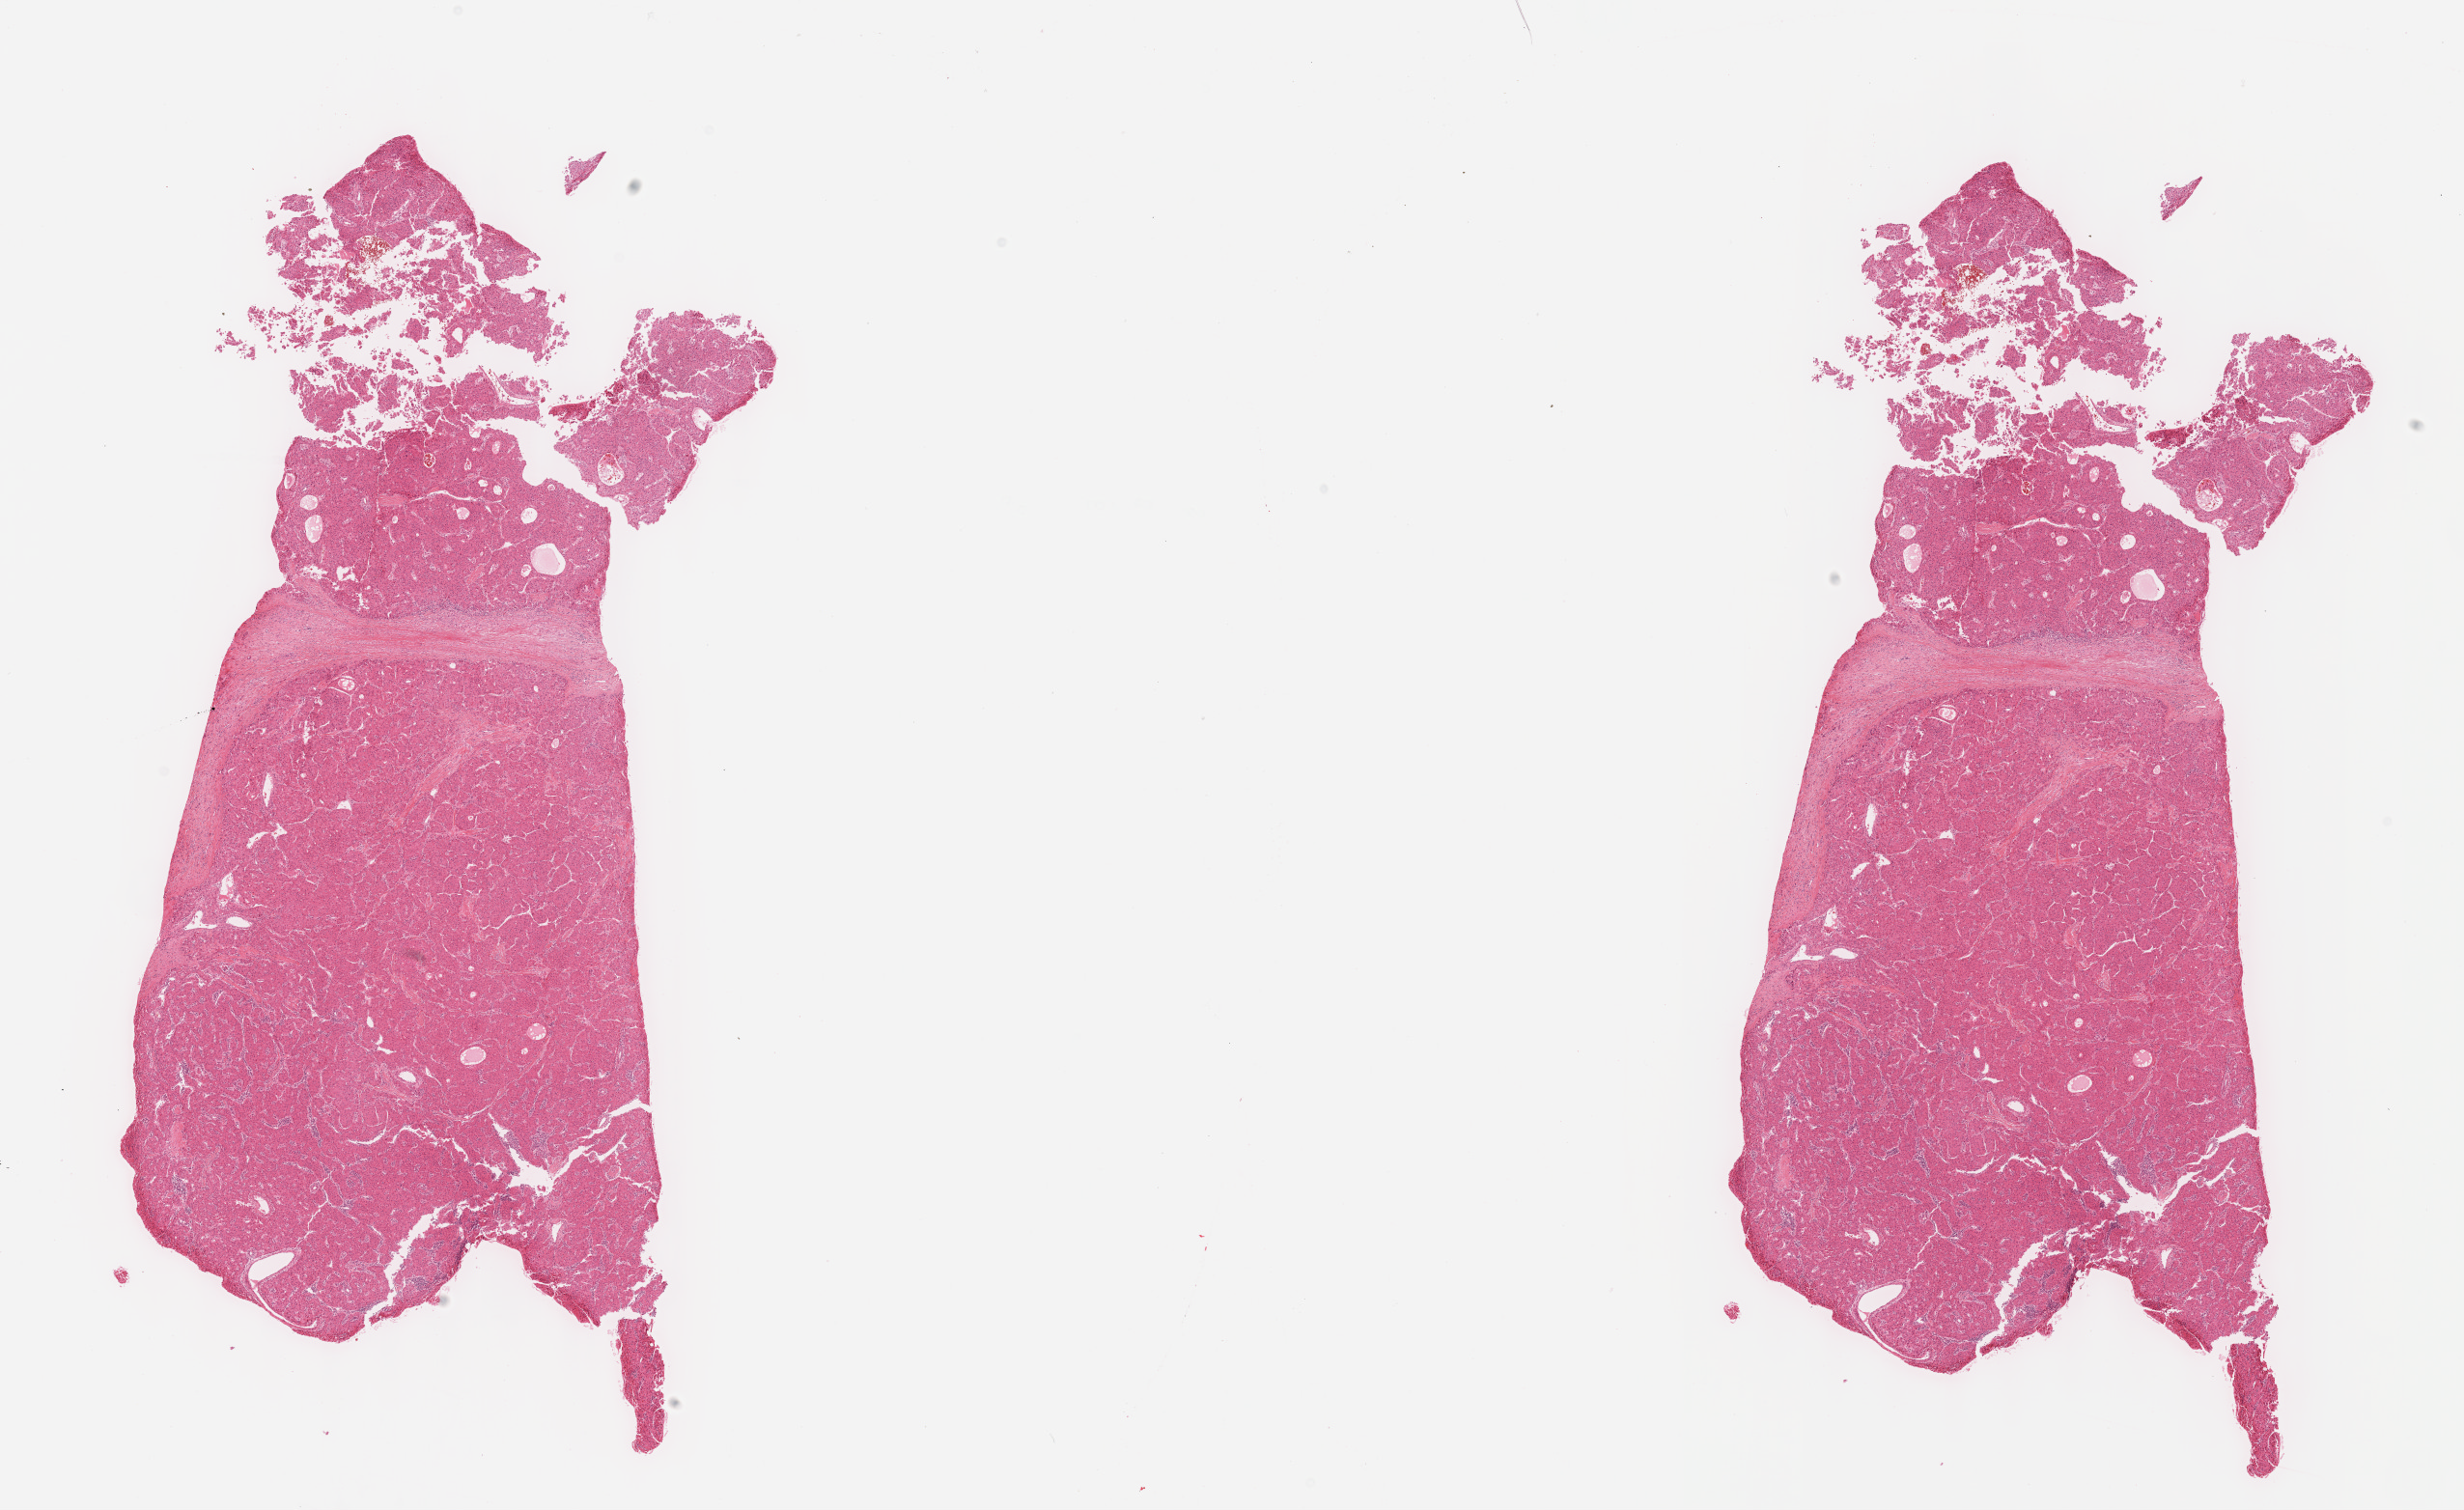
H&E whole-slide image — a low-resolution overview of the entire scanned area, about 20.6 x 12.6 mm, FFPE section, primary tumour sample from the liver. Male patient; age at initial diagnosis 58 years. Histologic grade: G3 (poorly differentiated).
AJCC pathologic stage: II. Diagnosis: Hepatocellular carcinoma, NOS.